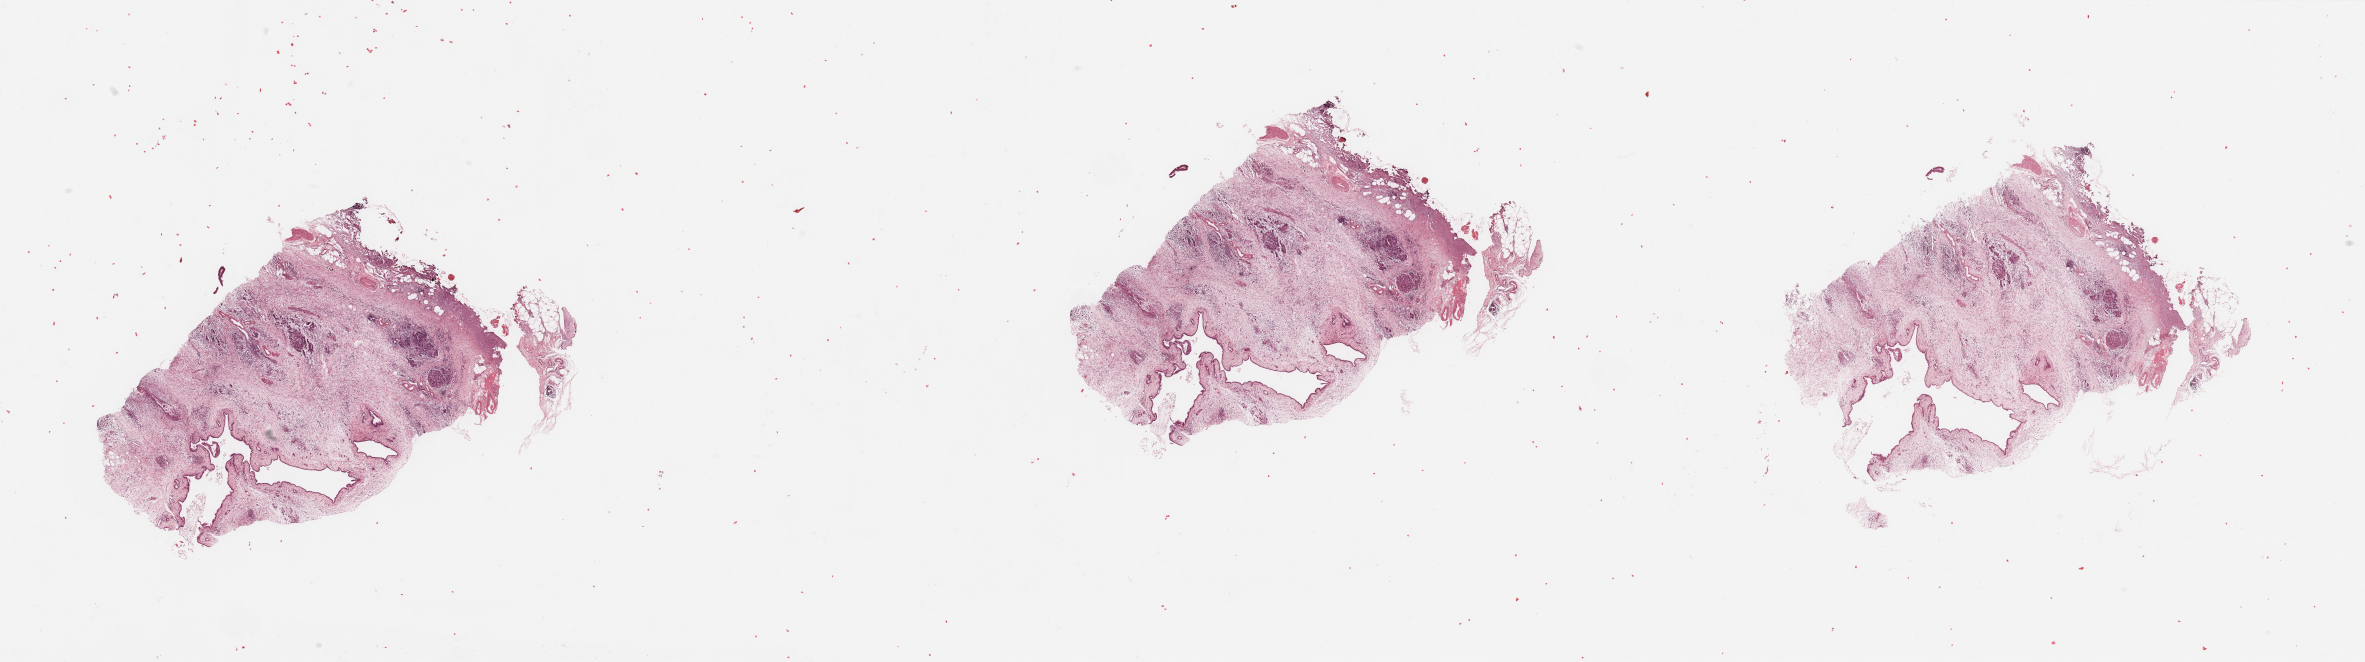
Digitized H&E tissue section (whole slide) — a low-resolution overview of the entire scanned area, about 37.4 x 10.5 mm (from a 20x scan); pancreas, normal (non-tumour) tissue. Female, 56 y/o.
This section: normal (non-tumour) tissue from the same patient. Patient diagnosis: Infiltrating duct carcinoma, NOS.